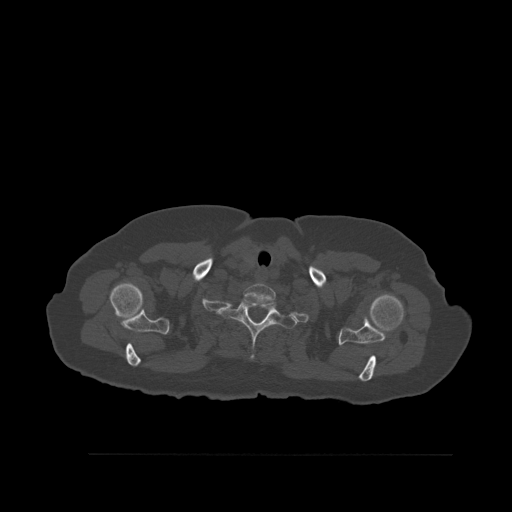
CT including the spine, one axial slice. Position 445 of 527 along the scan axis. Bone window (W 1800 / L 400 HU). 1.5 mm slice thickness. 512 × 512 image matrix, field of view 470 × 470 mm. Female patient, age 73 years. Case-level facts recorded for this patient, not image findings: primary cancer: breast.
Outlined on this slice (semi-automatically segmented with operator editing):
- T1 vertebra: bounding box (x1, y1, x2, y2) in pixels: (219, 298, 298, 360)